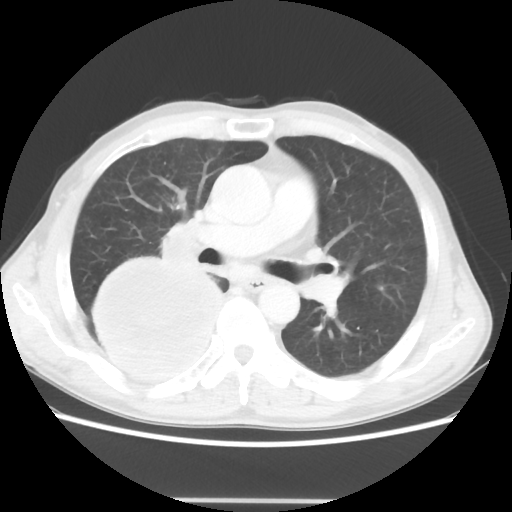
Chest CT, one axial slice; slice 28 of 48 in the series (ordered by position); reconstruction kernel STANDARD; 100 kVp; lung window (W 1500 / L -600 HU); 5 mm slice thickness; 512 × 512 image matrix. Patient: male, 66 years. Case-level facts recorded for this patient, not image findings: clinical TNM (as recorded): T4 N1 M1; histopathological grade: G3.
Annotated regions visible in this slice (bounding box drawn by a radiologist):
- lung tumour (recorded histology: small cell carcinoma): bounding box <81,257,231,392> (left, top, right, bottom; pixels)